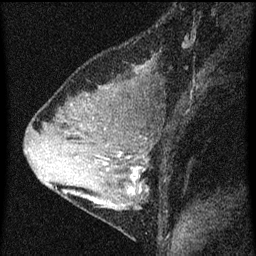
Breast MRI (dynamic contrast-enhanced), one sagittal slice; dynamic contrast-enhanced series, image 2 of 3 at this slice position (ordered by acquisition); 1.5 T; TE 4.2 ms, TR 8 ms; 2 mm slice thickness; 256 × 256 image matrix. Female patient, age 33 years.
Structures marked on this image (semi-automatically segmented with operator editing):
- analysis volume of interest (the breast-tissue region the enhancement analysis was run in; not a lesion): bounding box [x1, y1, x2, y2] px = [67, 118, 160, 215]
- tumour enhancement mask (voxels above the 70 % enhancement threshold inside the analysis volume of interest): [93, 152, 147, 205]